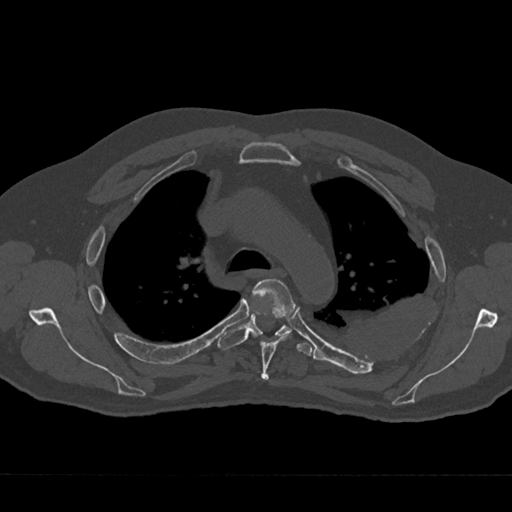
CT including the spine, one axial slice. Position 499 of 797 along the scan axis. Reconstruction kernel Br40s/3. 120 kVp. Bone window (W 1800 / L 400 HU). 0.5 mm slice thickness. 512 × 512 image matrix, field of view 377 × 377 mm. Male patient, age 75 years. Case-level facts recorded for this patient, not image findings: primary cancer: renal.
Outlined on this slice (semi-automatically segmented with operator editing):
- T4 vertebra: bounding box <252,278,295,380> (left, top, right, bottom; pixels)
- T5 vertebra: <218,314,312,356>